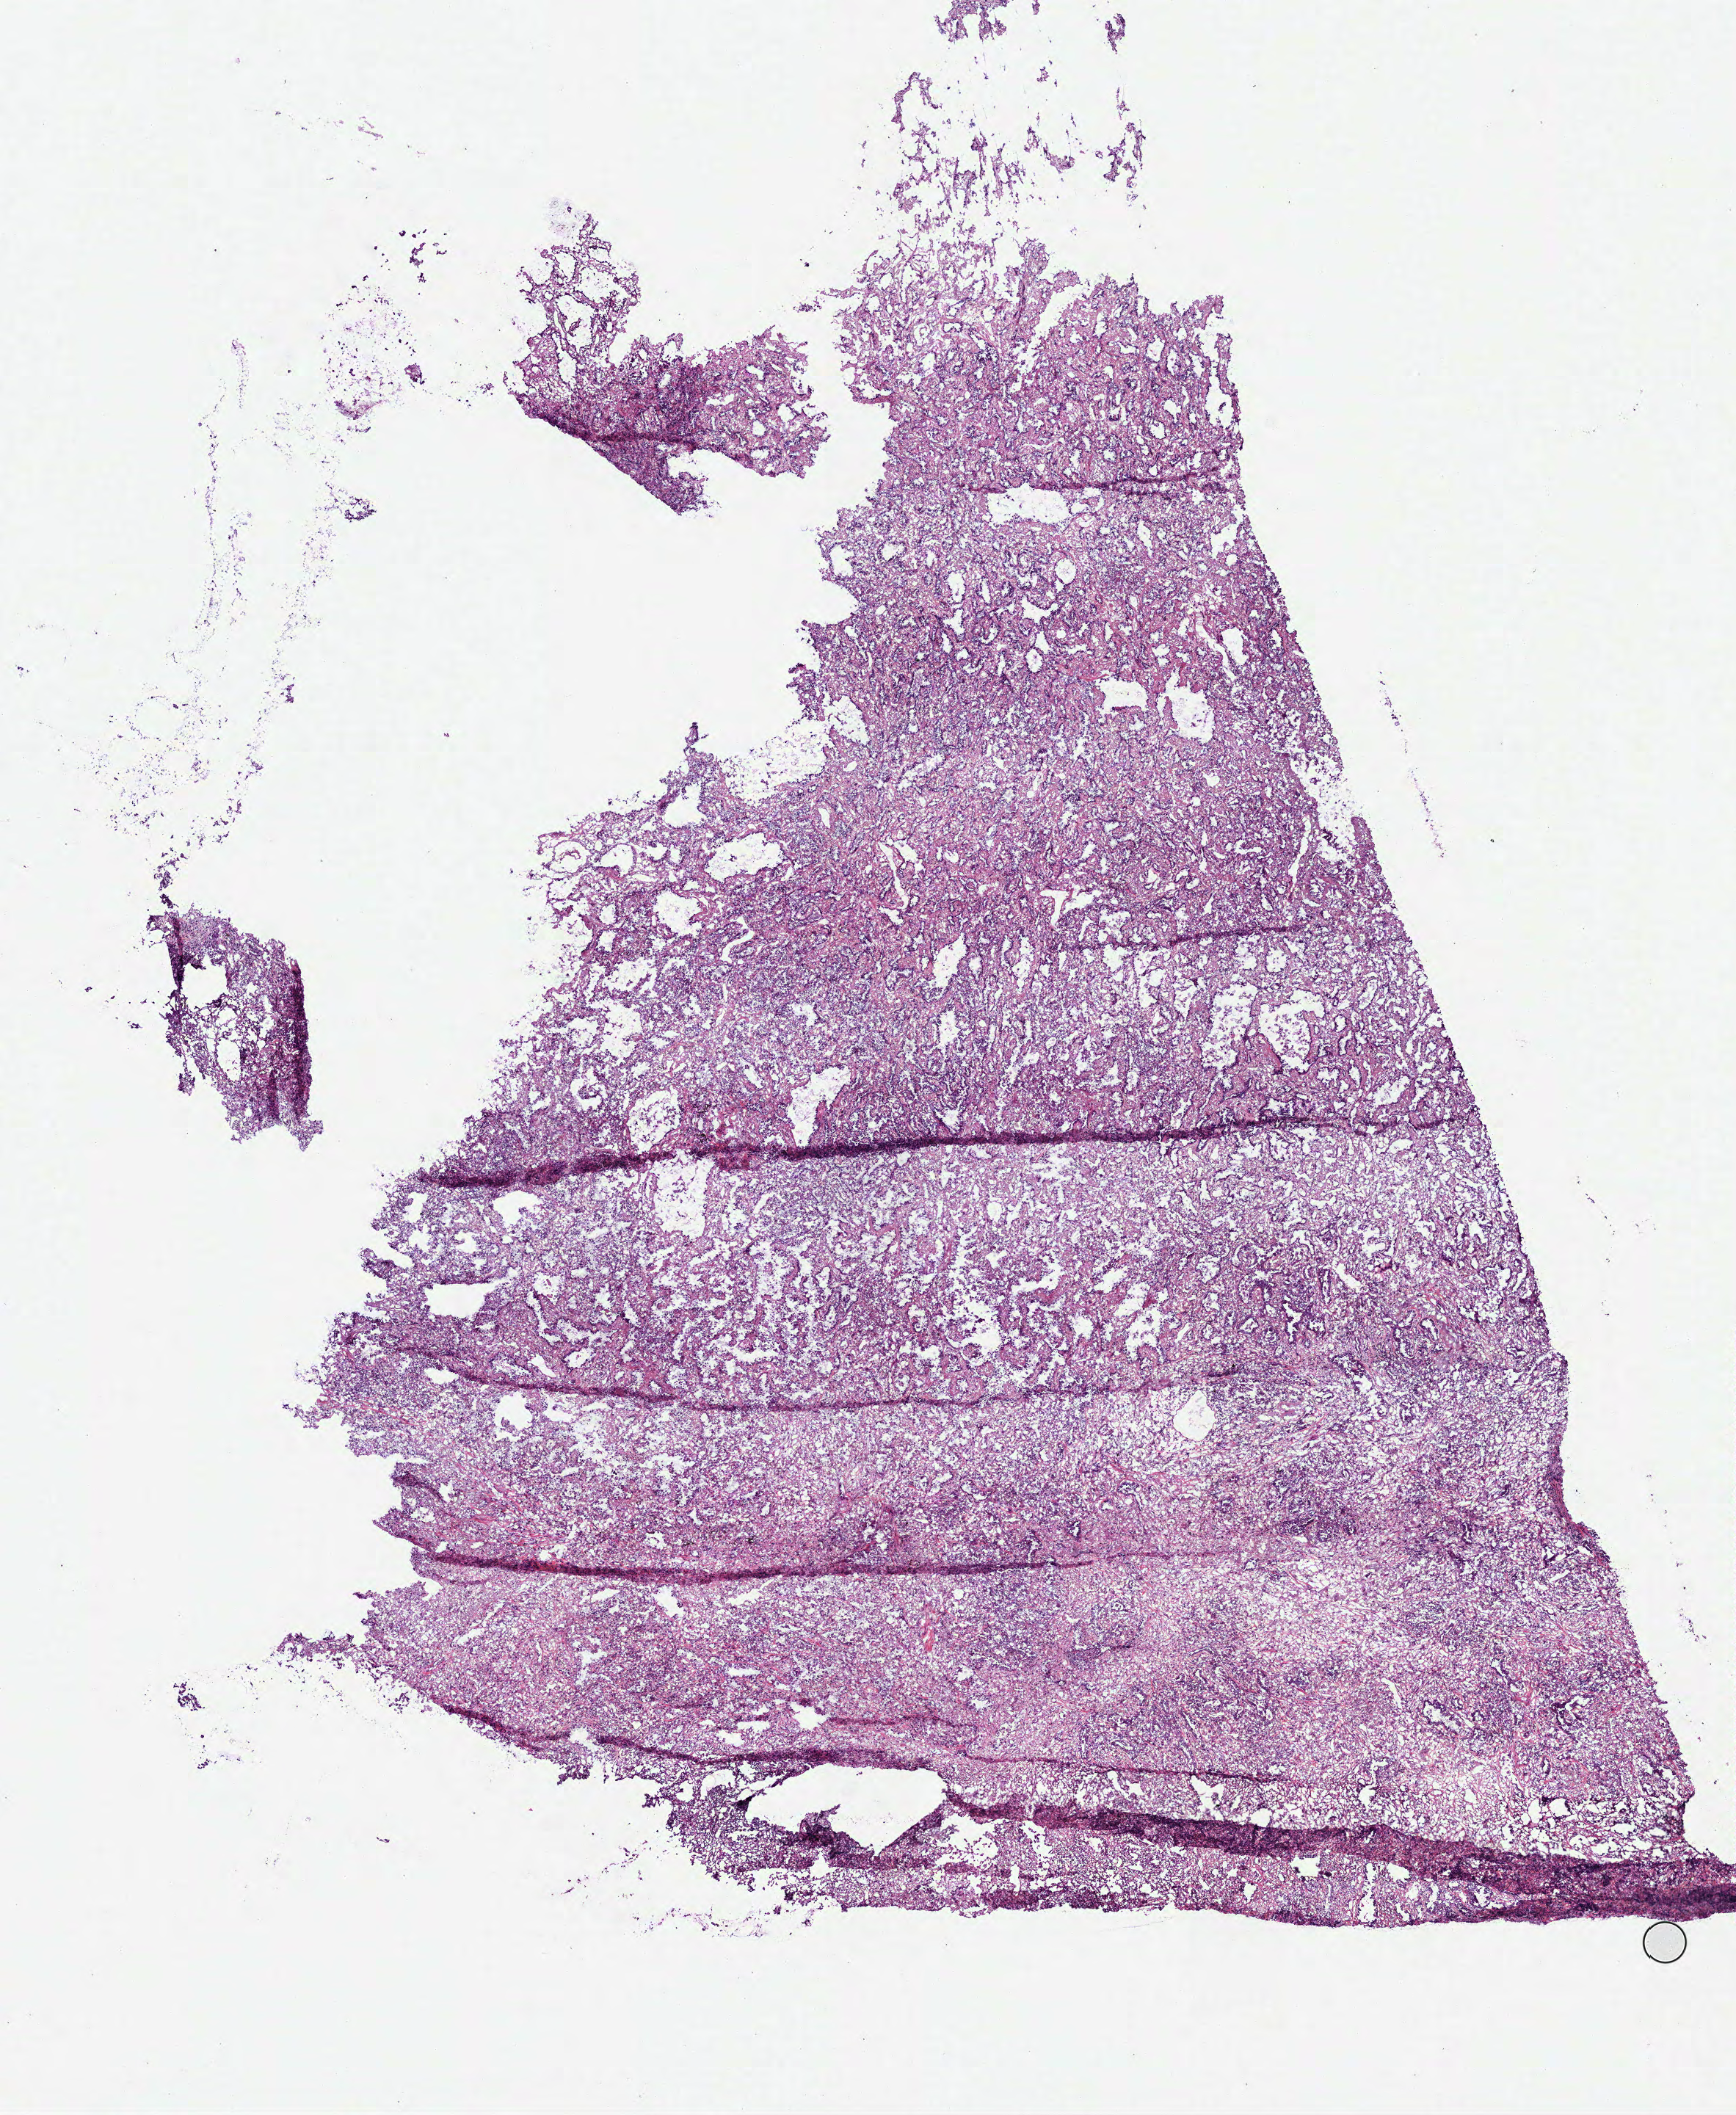
Hematoxylin and eosin (H&E) stained whole-slide image, a low-resolution overview of the entire scanned area, about 9.5 x 11.6 mm (acquisition: 40x scan). Frozen section from the top of the tissue portion. Primary tumour sample from the lung. Female, age 86 years at initial diagnosis. Slide review estimates, as recorded: tumour cells 100%, tumour nuclei 80%, normal cells 0%, stromal cells 0%, necrosis 0%. Infiltration values recorded for this section: lymphocyte infiltration 5%, monocyte infiltration 1%, neutrophil infiltration 2%.
Laterality: left. Pathologic diagnosis: Adenocarcinoma, NOS (upper lobe, lung). TNM: T1 N0 M0. AJCC pathologic stage: IA (6th edition).